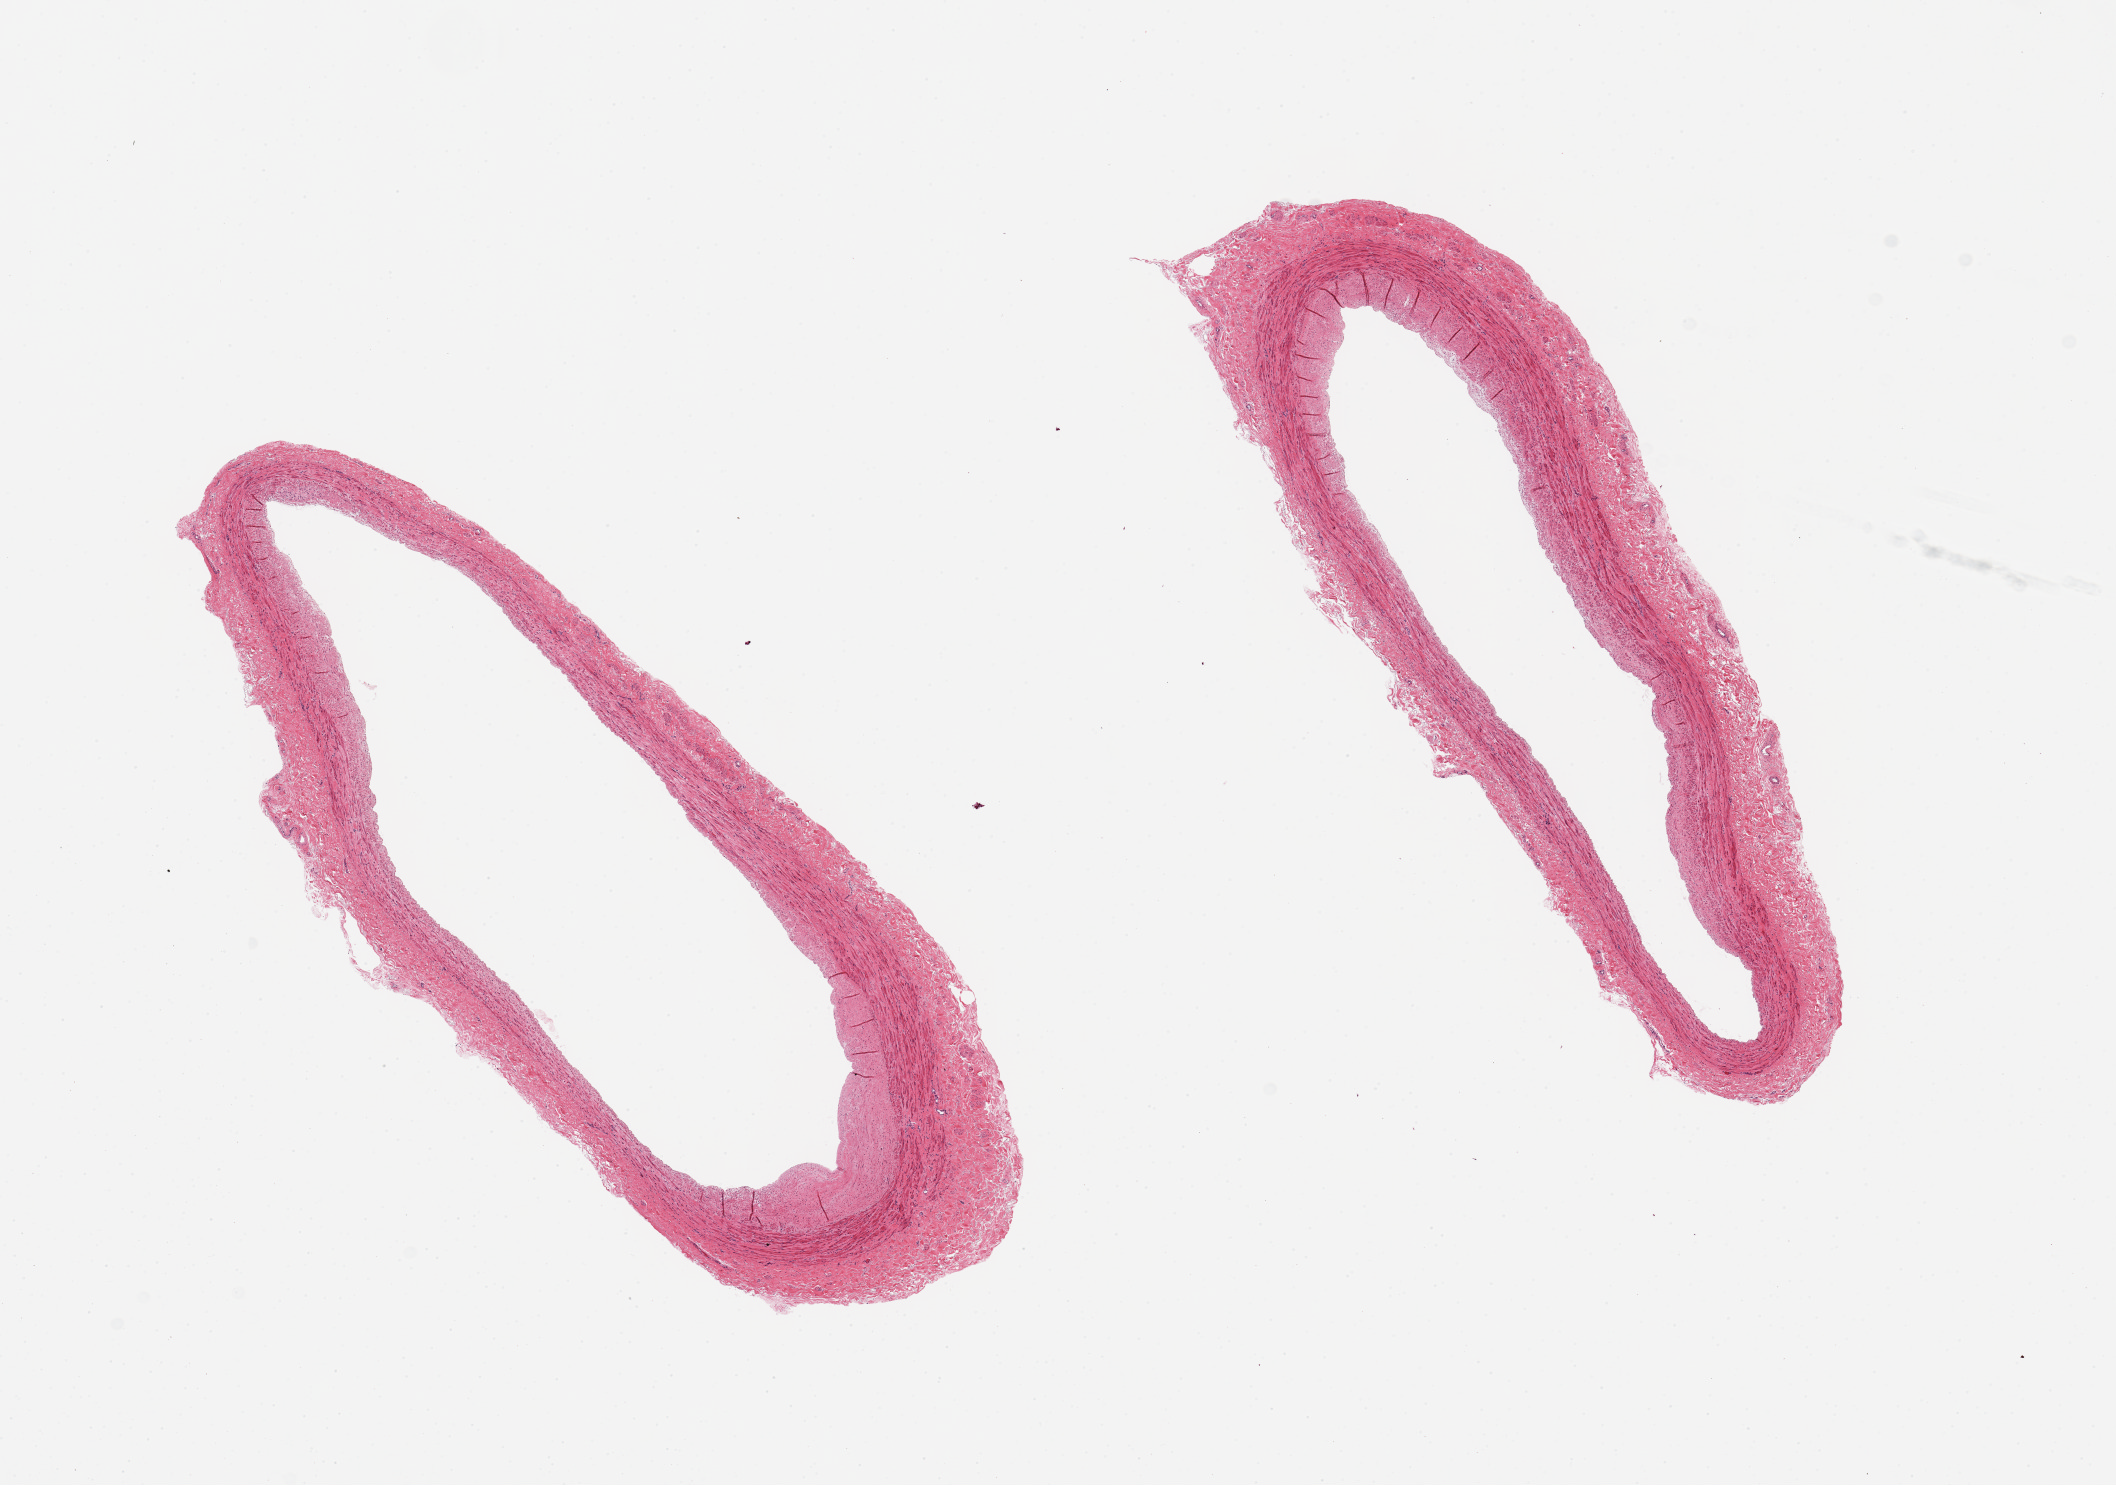
H&E whole-slide image, whole scanned area (about 16.7 x 11.7 mm, slide scanned at 20x) shown as a low-resolution overview. PAXgene-fixed, paraffin-embedded tissue. Target tissue: tibial artery. Donor tissue sample. Male donor.
- review note (as recorded): 2 pieces; well trimmed, mild atherosclerosis